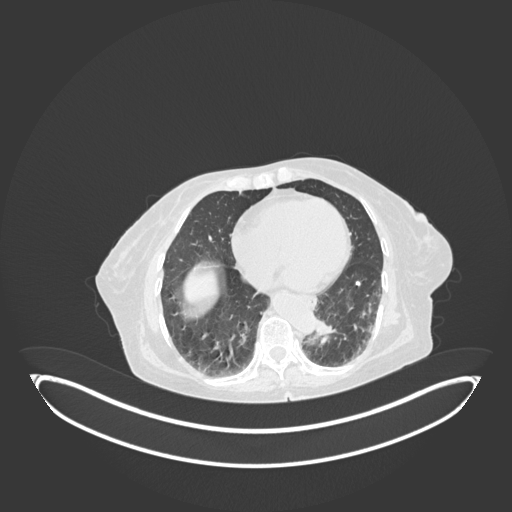
Chest CT, one axial slice. Slice 24 of 189 in the series (ordered by position). Reconstruction kernel B30f. Lung window (W 1500 / L -600 HU). 1 mm slice thickness. 512 × 512 image matrix. Patient: female, 82 years. Case-level facts recorded for this patient, not image findings: clinical TNM (as recorded): T1b N0 M1.
Annotated regions visible in this slice (bounding box drawn by a radiologist):
- lung tumour (recorded histology: adenocarcinoma): bounding box [x1, y1, x2, y2] px = [312, 318, 336, 346]